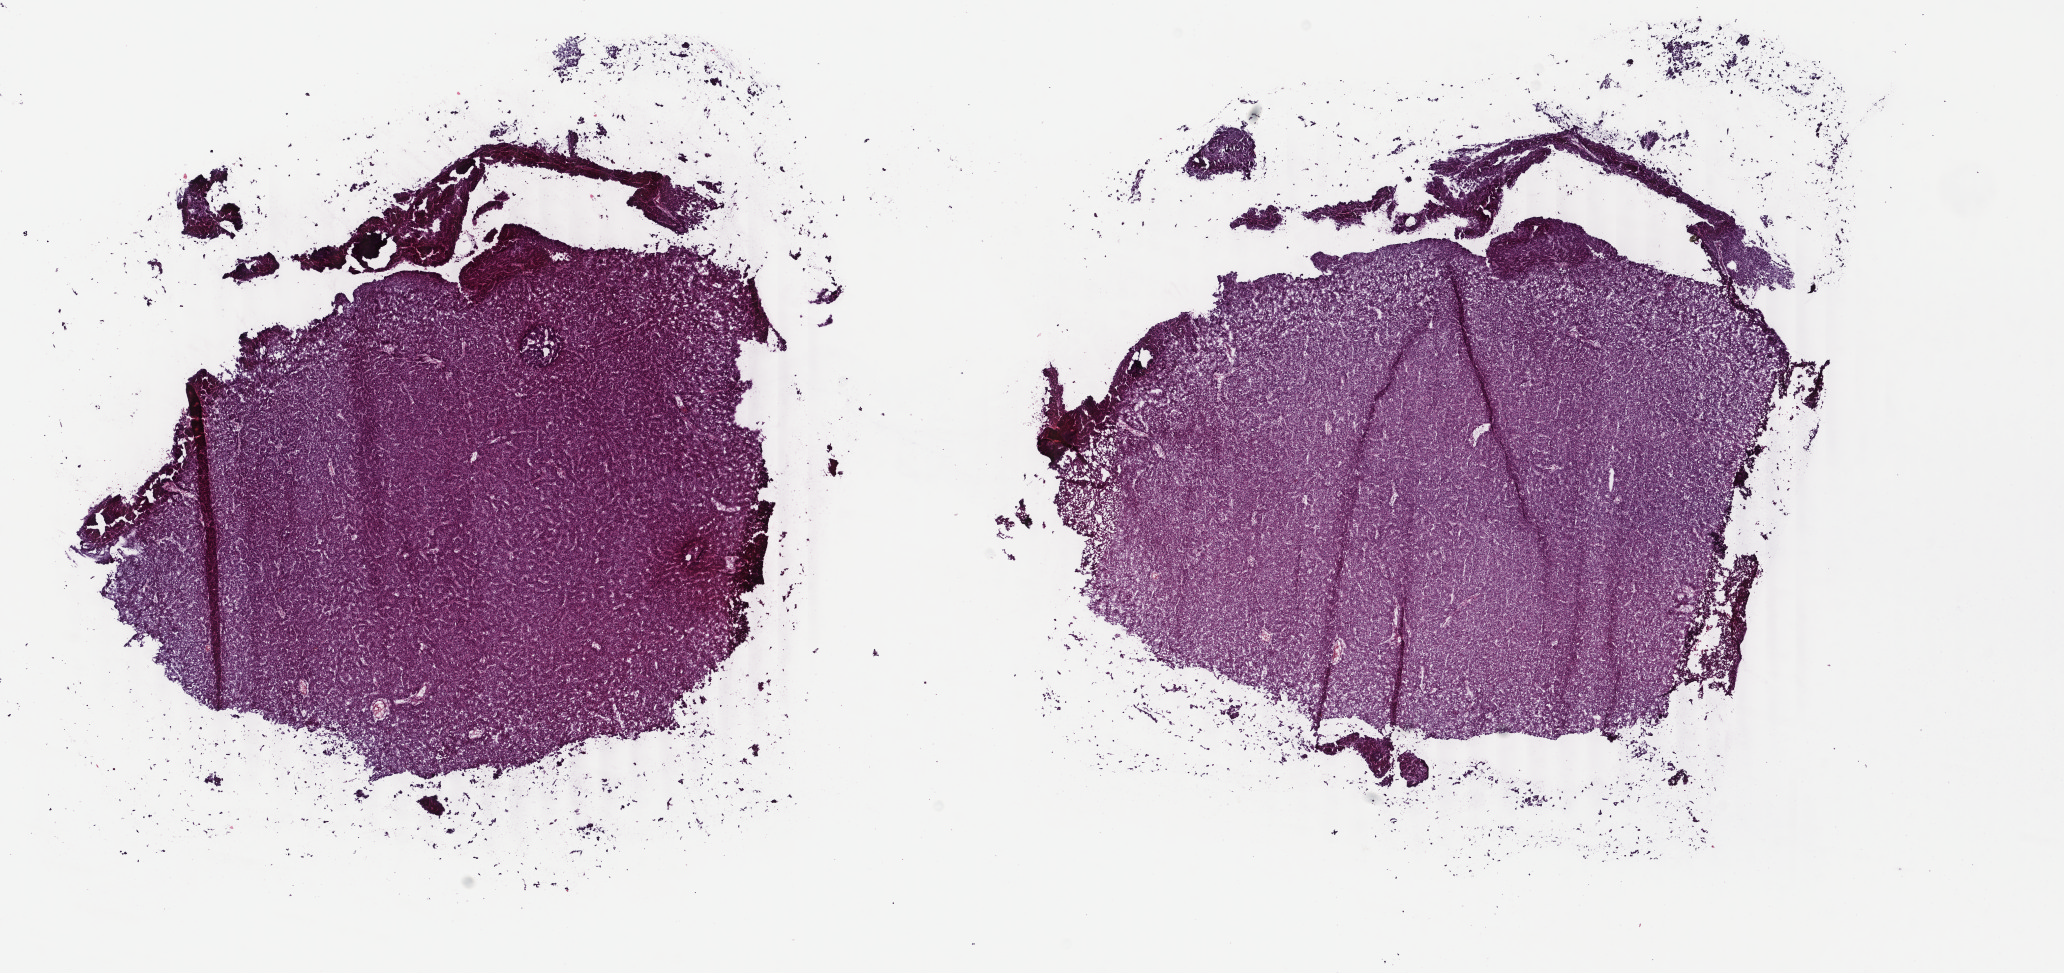
Digitized Hematoxylin and eosin (H&E) stained tissue section (whole slide), shown as a low-resolution overview of the whole scanned area (about 16.4 x 7.7 mm), frozen section from the top of the tissue portion, sample: primary tumour, liver. Male, age 73 years at initial diagnosis.
Pathologic diagnosis: Hepatocellular carcinoma, NOS.